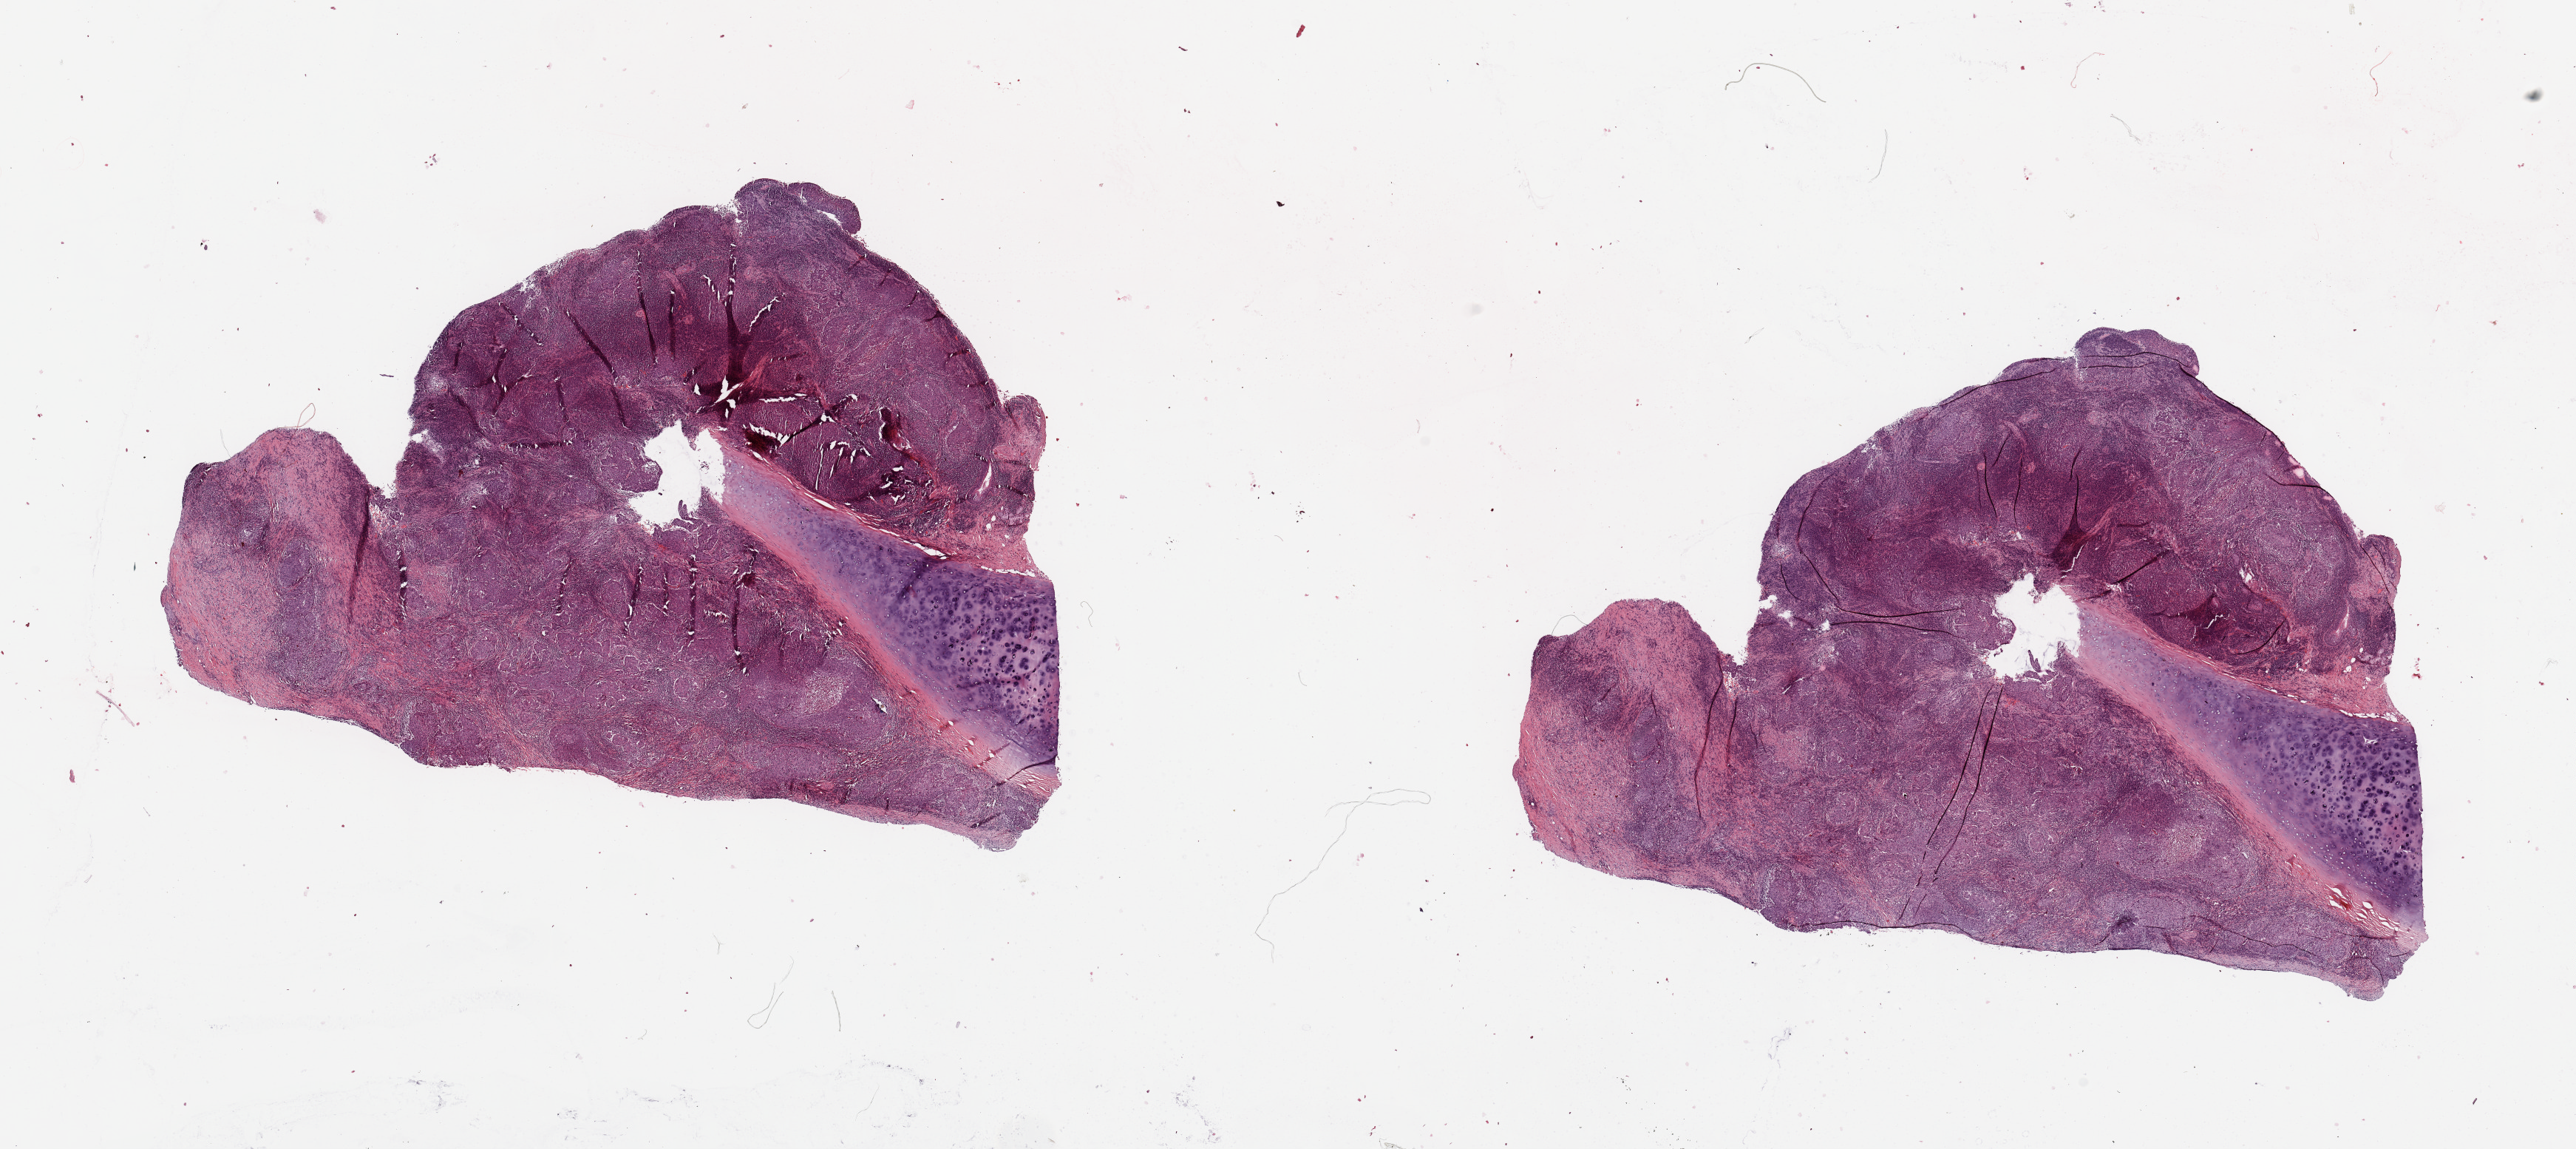
Digitized Hematoxylin and eosin (H&E) stained tissue section (whole slide), shown as a low-resolution overview of the whole scanned area (about 27.6 x 12.3 mm). Lung, tumour tissue. Male, 66 y/o. Histologic grade: G3 (poorly differentiated).
* diagnosis: Squamous cell carcinoma, NOS
* AJCC pathologic stage: IIA